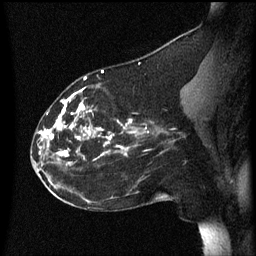
Breast MRI (dynamic contrast-enhanced), one sagittal slice; slice 25 of 60 in the series (ordered by position); dynamic contrast-enhanced series, image 2 of 3 at this slice position (ordered by acquisition); 1.5 T; TE 4.2 ms, TR 8.4 ms; 2.2 mm slice thickness; 256 × 256 image matrix. Patient: female, 35 years. Case-level facts recorded for this patient, not image findings: setting: breast cancer imaged before/during neoadjuvant chemotherapy; receptor status: HER2-positive.
Outlined on this slice (semi-automatic segmentation, software-assisted and operator-edited):
- analysis volume of interest (the breast-tissue region the enhancement analysis was run in; not a lesion): bounding box (x1, y1, x2, y2) in pixels: (32, 72, 178, 173)
- tumour enhancement mask (voxels above the 70 % enhancement threshold inside the analysis volume of interest): (39, 72, 149, 165)